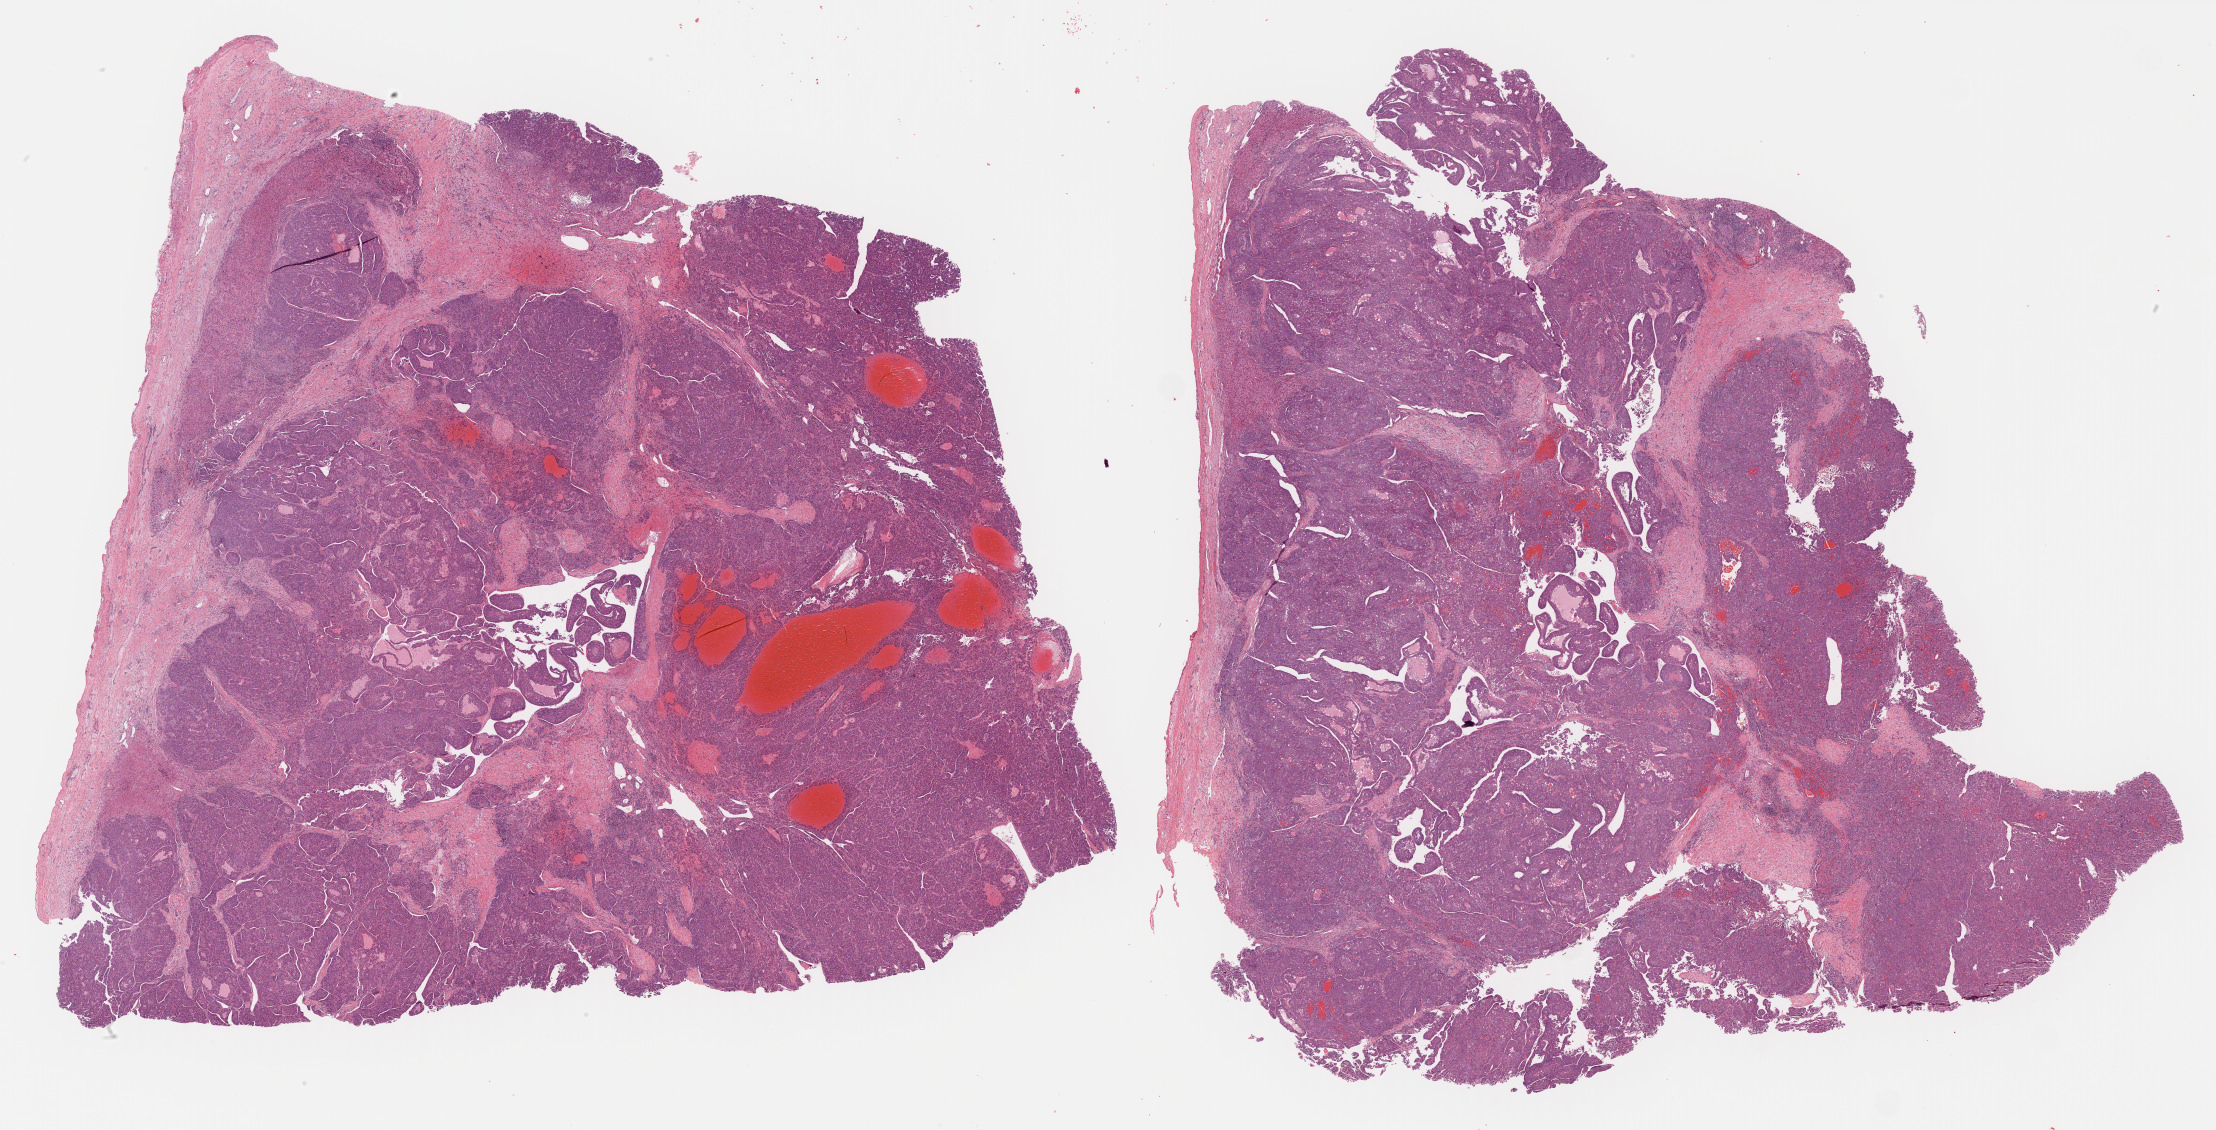
Hematoxylin and eosin (H&E) stained whole-slide image, low-resolution overview of the scanned area, about 35.9 x 18.3 mm (acquisition: 40x scan). Formalin-fixed paraffin-embedded (FFPE) diagnostic section. Liver, primary tumour sample. Female, age 85 years at initial diagnosis. Histologic grade: G3 (poorly differentiated).
AJCC pathologic stage: I (6th edition). TNM: T1 N0 M0. Diagnosis: Hepatocellular carcinoma, NOS.